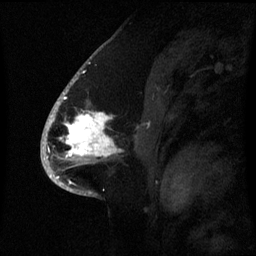
Breast MRI (dynamic contrast-enhanced), one sagittal slice. Slice 41 of 60 in the series (ordered by position). Dynamic contrast-enhanced series, image 2 of 3 at this slice position (ordered by acquisition). 1.5 T. TE 4.2 ms, TR 8.4 ms. 2.1 mm slice thickness. 256 × 256 image matrix. Patient: female, 53 years. Case-level facts recorded for this patient, not image findings: setting: breast cancer imaged before/during neoadjuvant chemotherapy; receptor status: HR-positive, HER2-negative.
Structures marked on this image (semi-automatic segmentation, software-assisted and operator-edited):
- analysis volume of interest (the breast-tissue region the enhancement analysis was run in; not a lesion): bounding box <52,90,120,171> (left, top, right, bottom; pixels)
- tumour enhancement mask (voxels above the 70 % enhancement threshold inside the analysis volume of interest): <52,102,115,159>